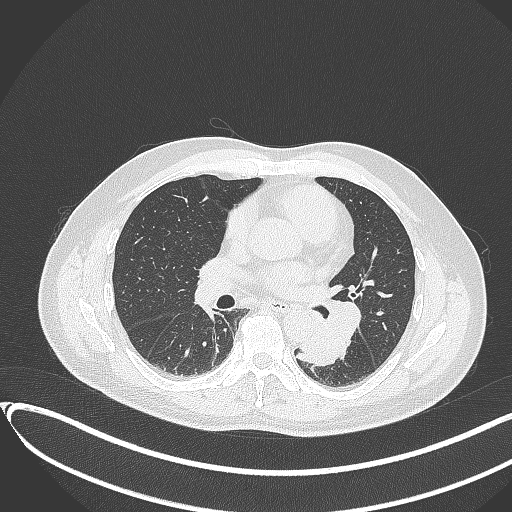
Chest CT, one axial slice. 120 kVp. Lung window (W 1500 / L -600 HU). 1 mm slice thickness. 512 × 512 image matrix, field of view 400 × 400 mm. Patient: male, 54 years. Case-level facts recorded for this patient, not image findings: clinical TNM (as recorded): T3 N0 M0.
Structures marked on this image (rectangle marked by the reading radiologist):
- lung tumour (recorded histology: squamous cell carcinoma): bounding box (x1, y1, x2, y2) in pixels: (293, 313, 344, 368)